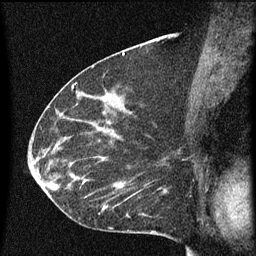
Breast MRI (dynamic contrast-enhanced), one sagittal slice; position 34 of 60 along the scan axis; dynamic contrast-enhanced series, image 2 of 3 at this slice position (ordered by acquisition); 1.5 T; TE 4.2 ms, TR 8 ms; 256 × 256 image matrix, field of view 180 × 180 mm. Patient: female, 55 years.
Annotated regions visible in this slice (semi-automatically segmented with operator editing):
- analysis volume of interest (the breast-tissue region the enhancement analysis was run in; not a lesion): bounding box [x1, y1, x2, y2] px = [51, 156, 145, 217]
- tumour enhancement mask (voxels above the 70 % enhancement threshold inside the analysis volume of interest): [52, 158, 144, 215]